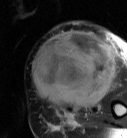
MRI of an extremity soft-tissue mass, one axial slice; slice 26 of 87 in the series (ordered by position); T2-weighted fat-saturated; MR volume resampled by the dataset authors to the PET/CT grid (not the native acquisition matrix); 127 × 138 image matrix. Female patient. Case-level facts recorded for this patient, not image findings: histological type: pleiomorphic leiomyosarcoma; grade: high; site of the primary tumour: left biceps.
Annotated regions visible in this slice (expert contour drawn on MRI and transferred to this co-registered scan by the dataset authors):
- gross tumour volume including surrounding oedema: bounding box <31,32,115,110> (left, top, right, bottom; pixels)
- gross tumour volume (mass): <31,32,115,110>